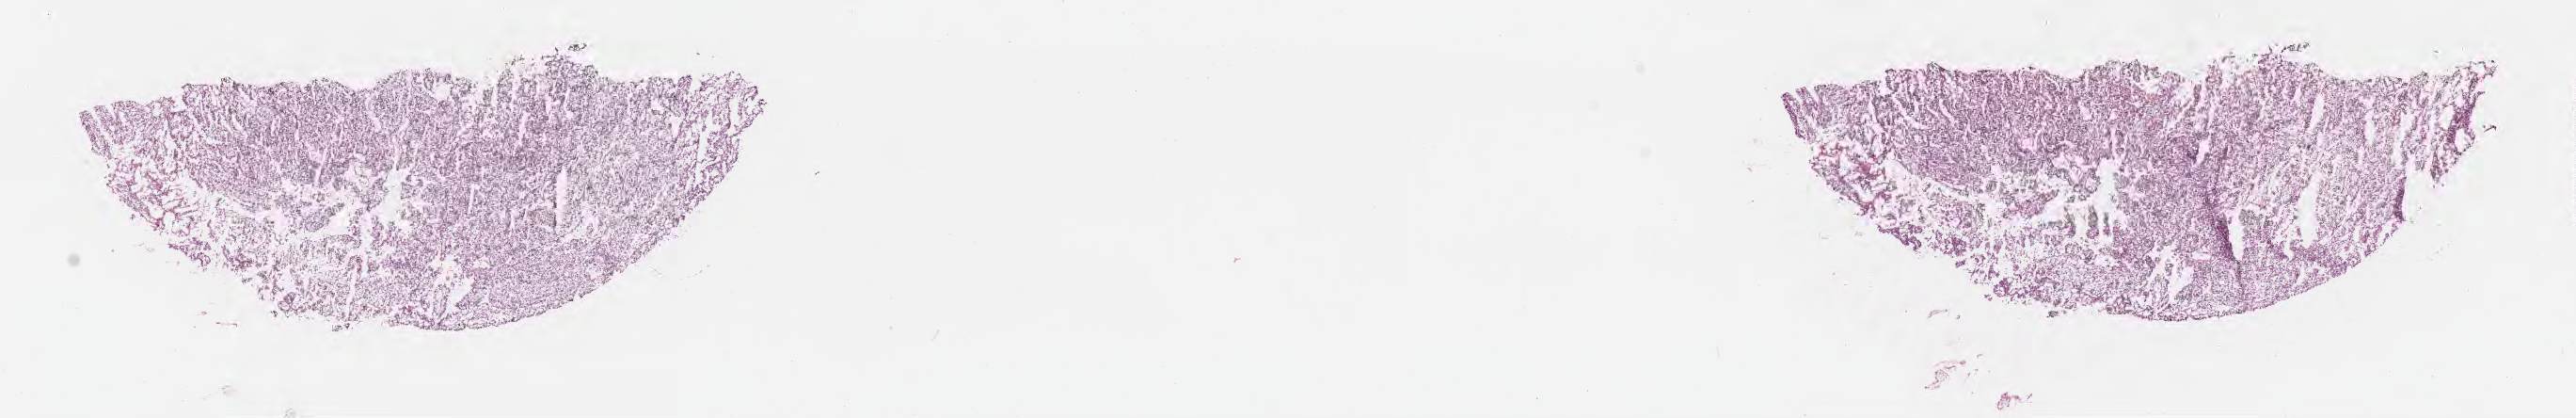
Haematoxylin and eosin whole-slide image, whole scanned area (about 22.1 x 3.6 mm) shown as a low-resolution overview; frozen section; primary tumor; site: kidney. Female patient; age at initial diagnosis 47 years. Tumor grade: G2 (moderately differentiated). Slide review estimates, as recorded: tumor cells 100%, tumor nuclei 98%, stromal cells 0%, necrosis 0%, normal cells 0%. Infiltration values recorded for this section: lymphocyte infiltration 0%, monocyte infiltration 0%, neutrophil infiltration 0%.
* diagnosis: Renal cell carcinoma, NOS
* section: top of the tissue portion
* AJCC pathologic stage: Stage III